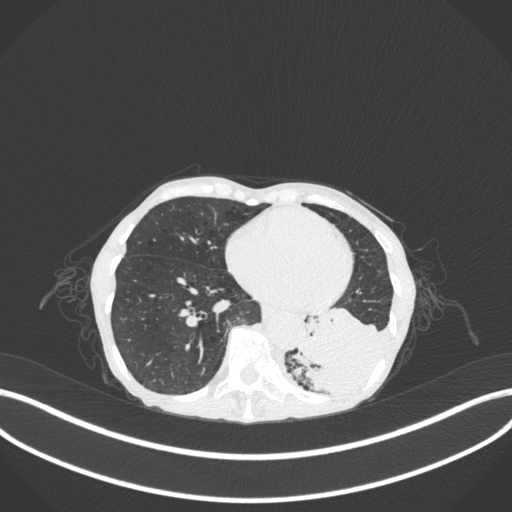
Chest CT, one axial slice. Position 84 of 347 along the scan axis. Lung window (W 1500 / L -600 HU). 1 mm slice thickness. 512 × 512 image matrix. Female patient, age 70 years. From the clinical record (not read from this slice): clinical TNM (as recorded): T3 N0 M0; histopathological grade: G3.
Outlined on this slice (rectangle marked by the reading radiologist):
- lung tumour (recorded histology: small cell carcinoma): bounding box (x1, y1, x2, y2) in pixels: (290, 300, 394, 399)